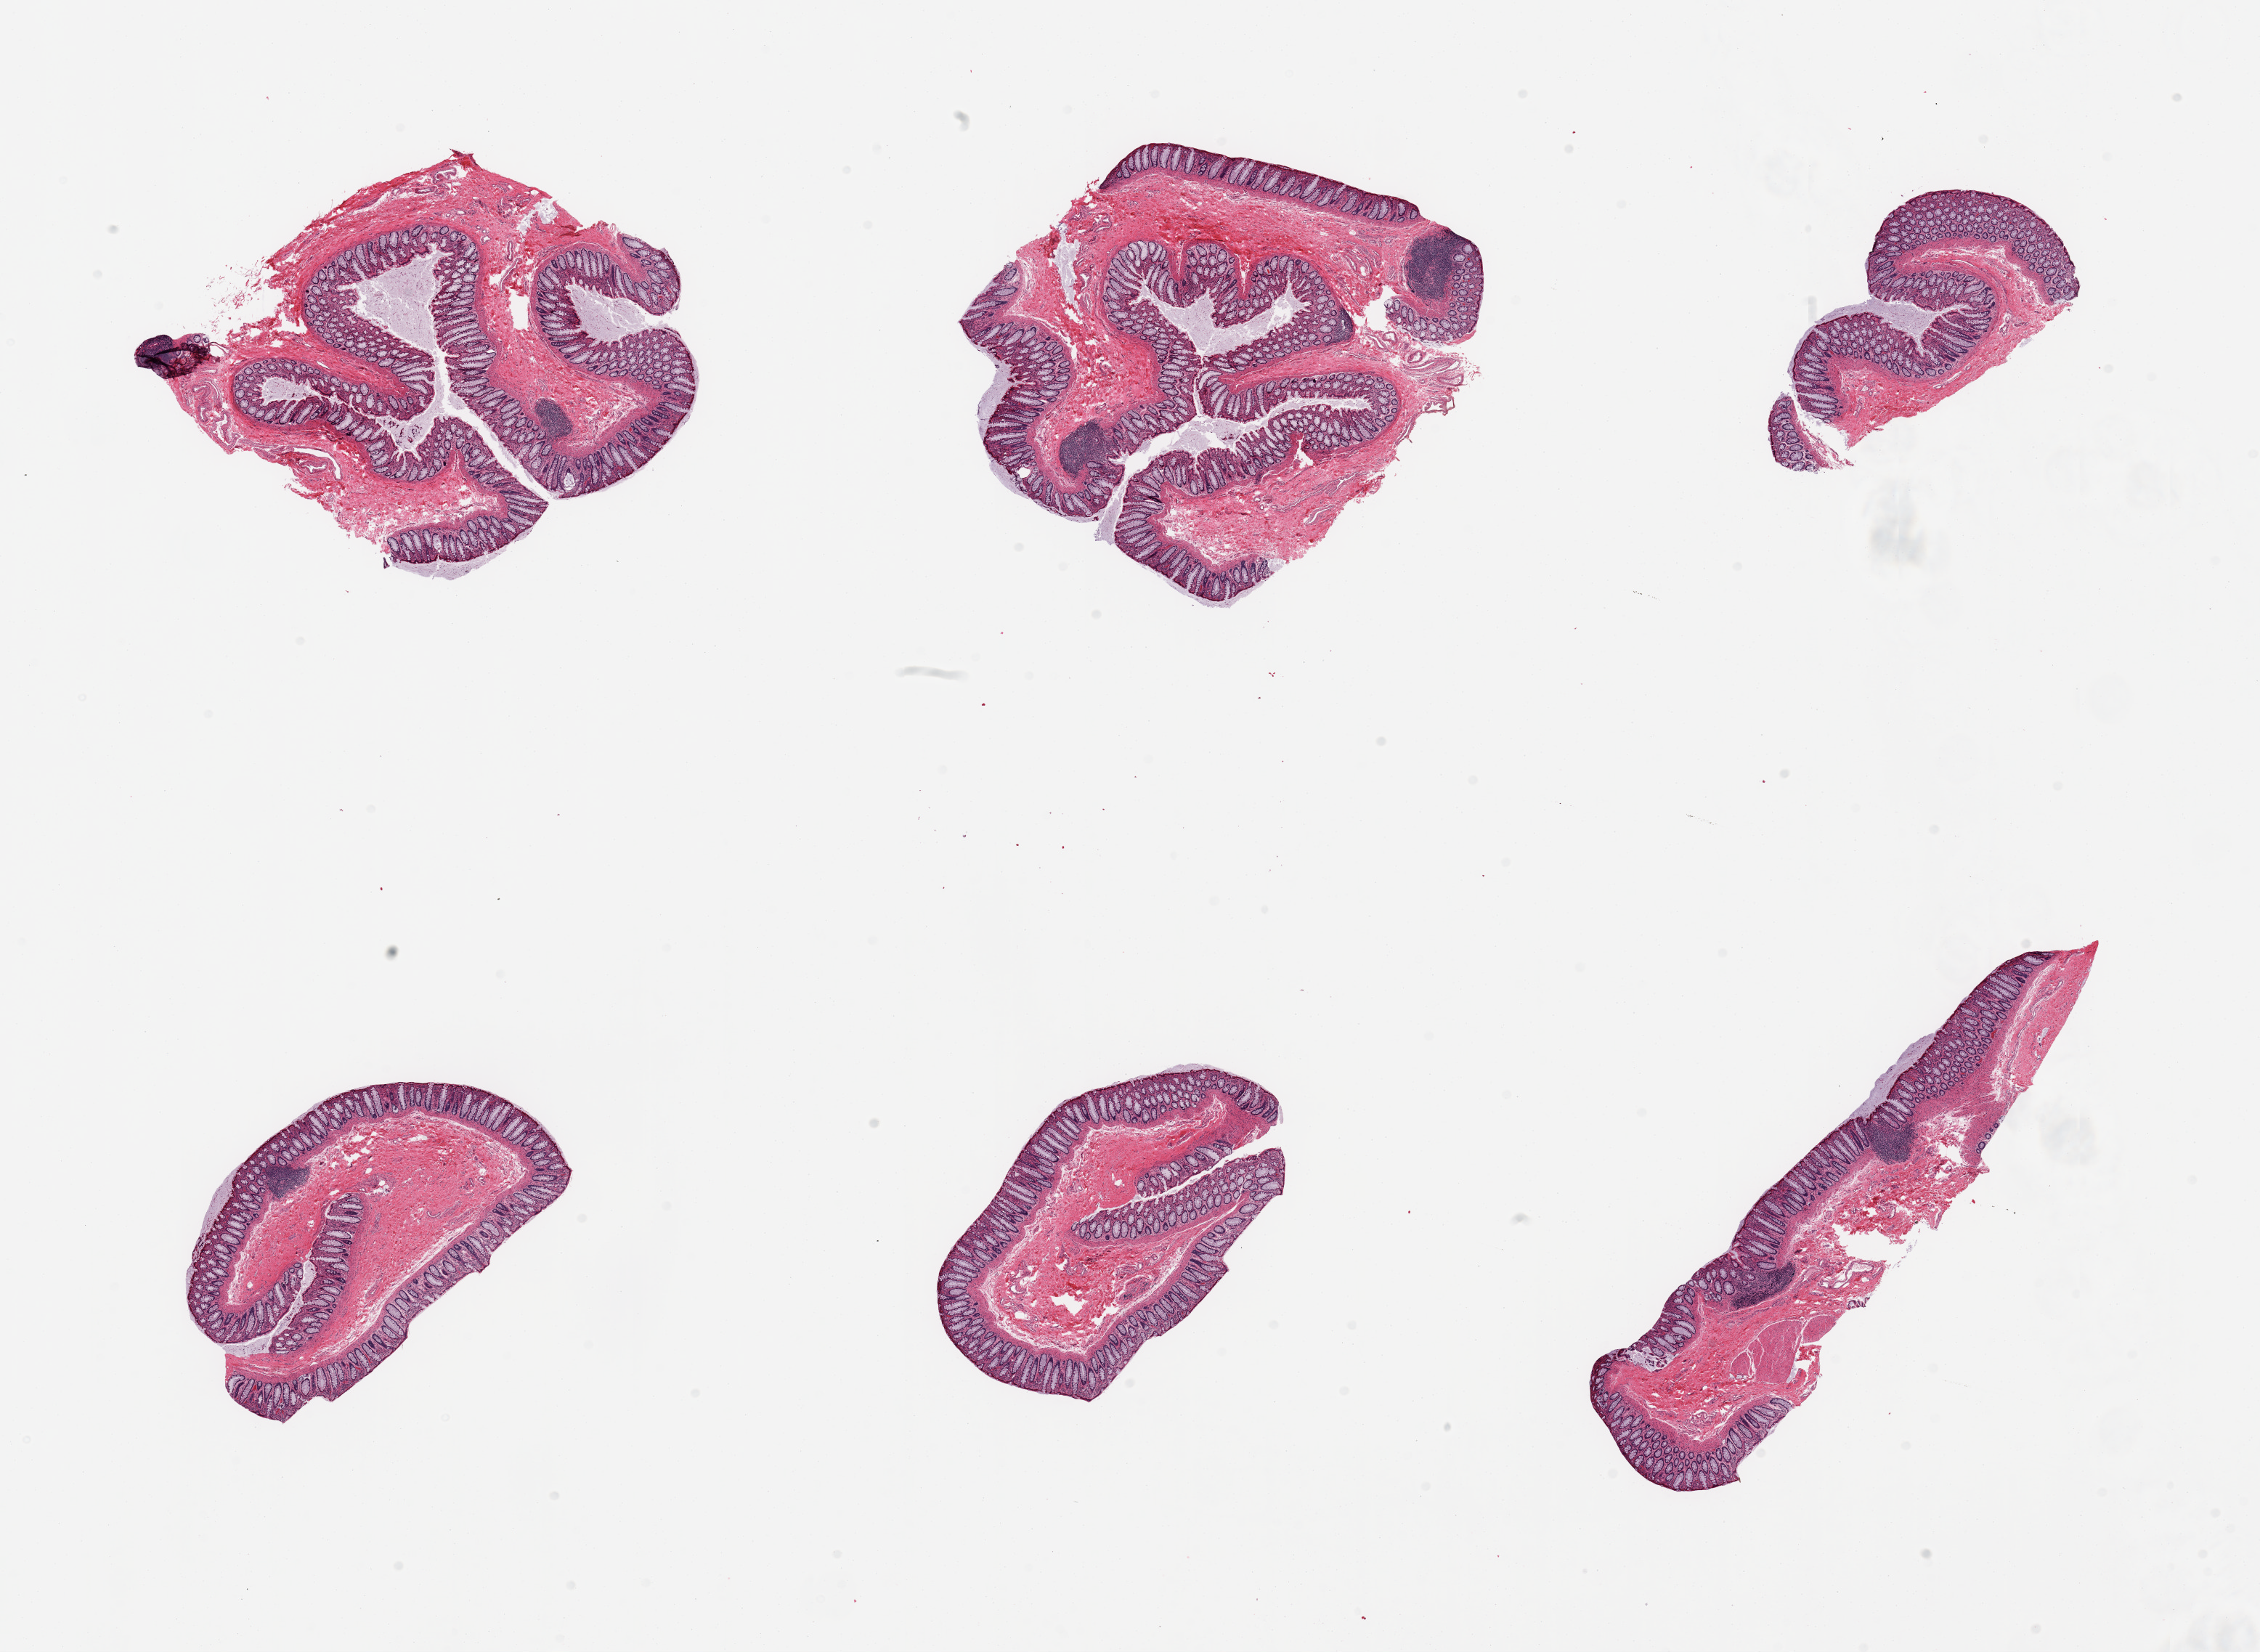
Whole-slide image, hematoxylin and eosin (H&E) stain — a low-resolution overview of the entire scanned area, about 24.6 x 18.0 mm (from a 20x scan). PAXgene-fixed paraffin-embedded (PFPE) section. Sampled site (target tissue): ileum. Tissue donor sample. Female donor.
Reviewer comment on this tissue sample: 6 pieces; colonic mucosa not ileum.